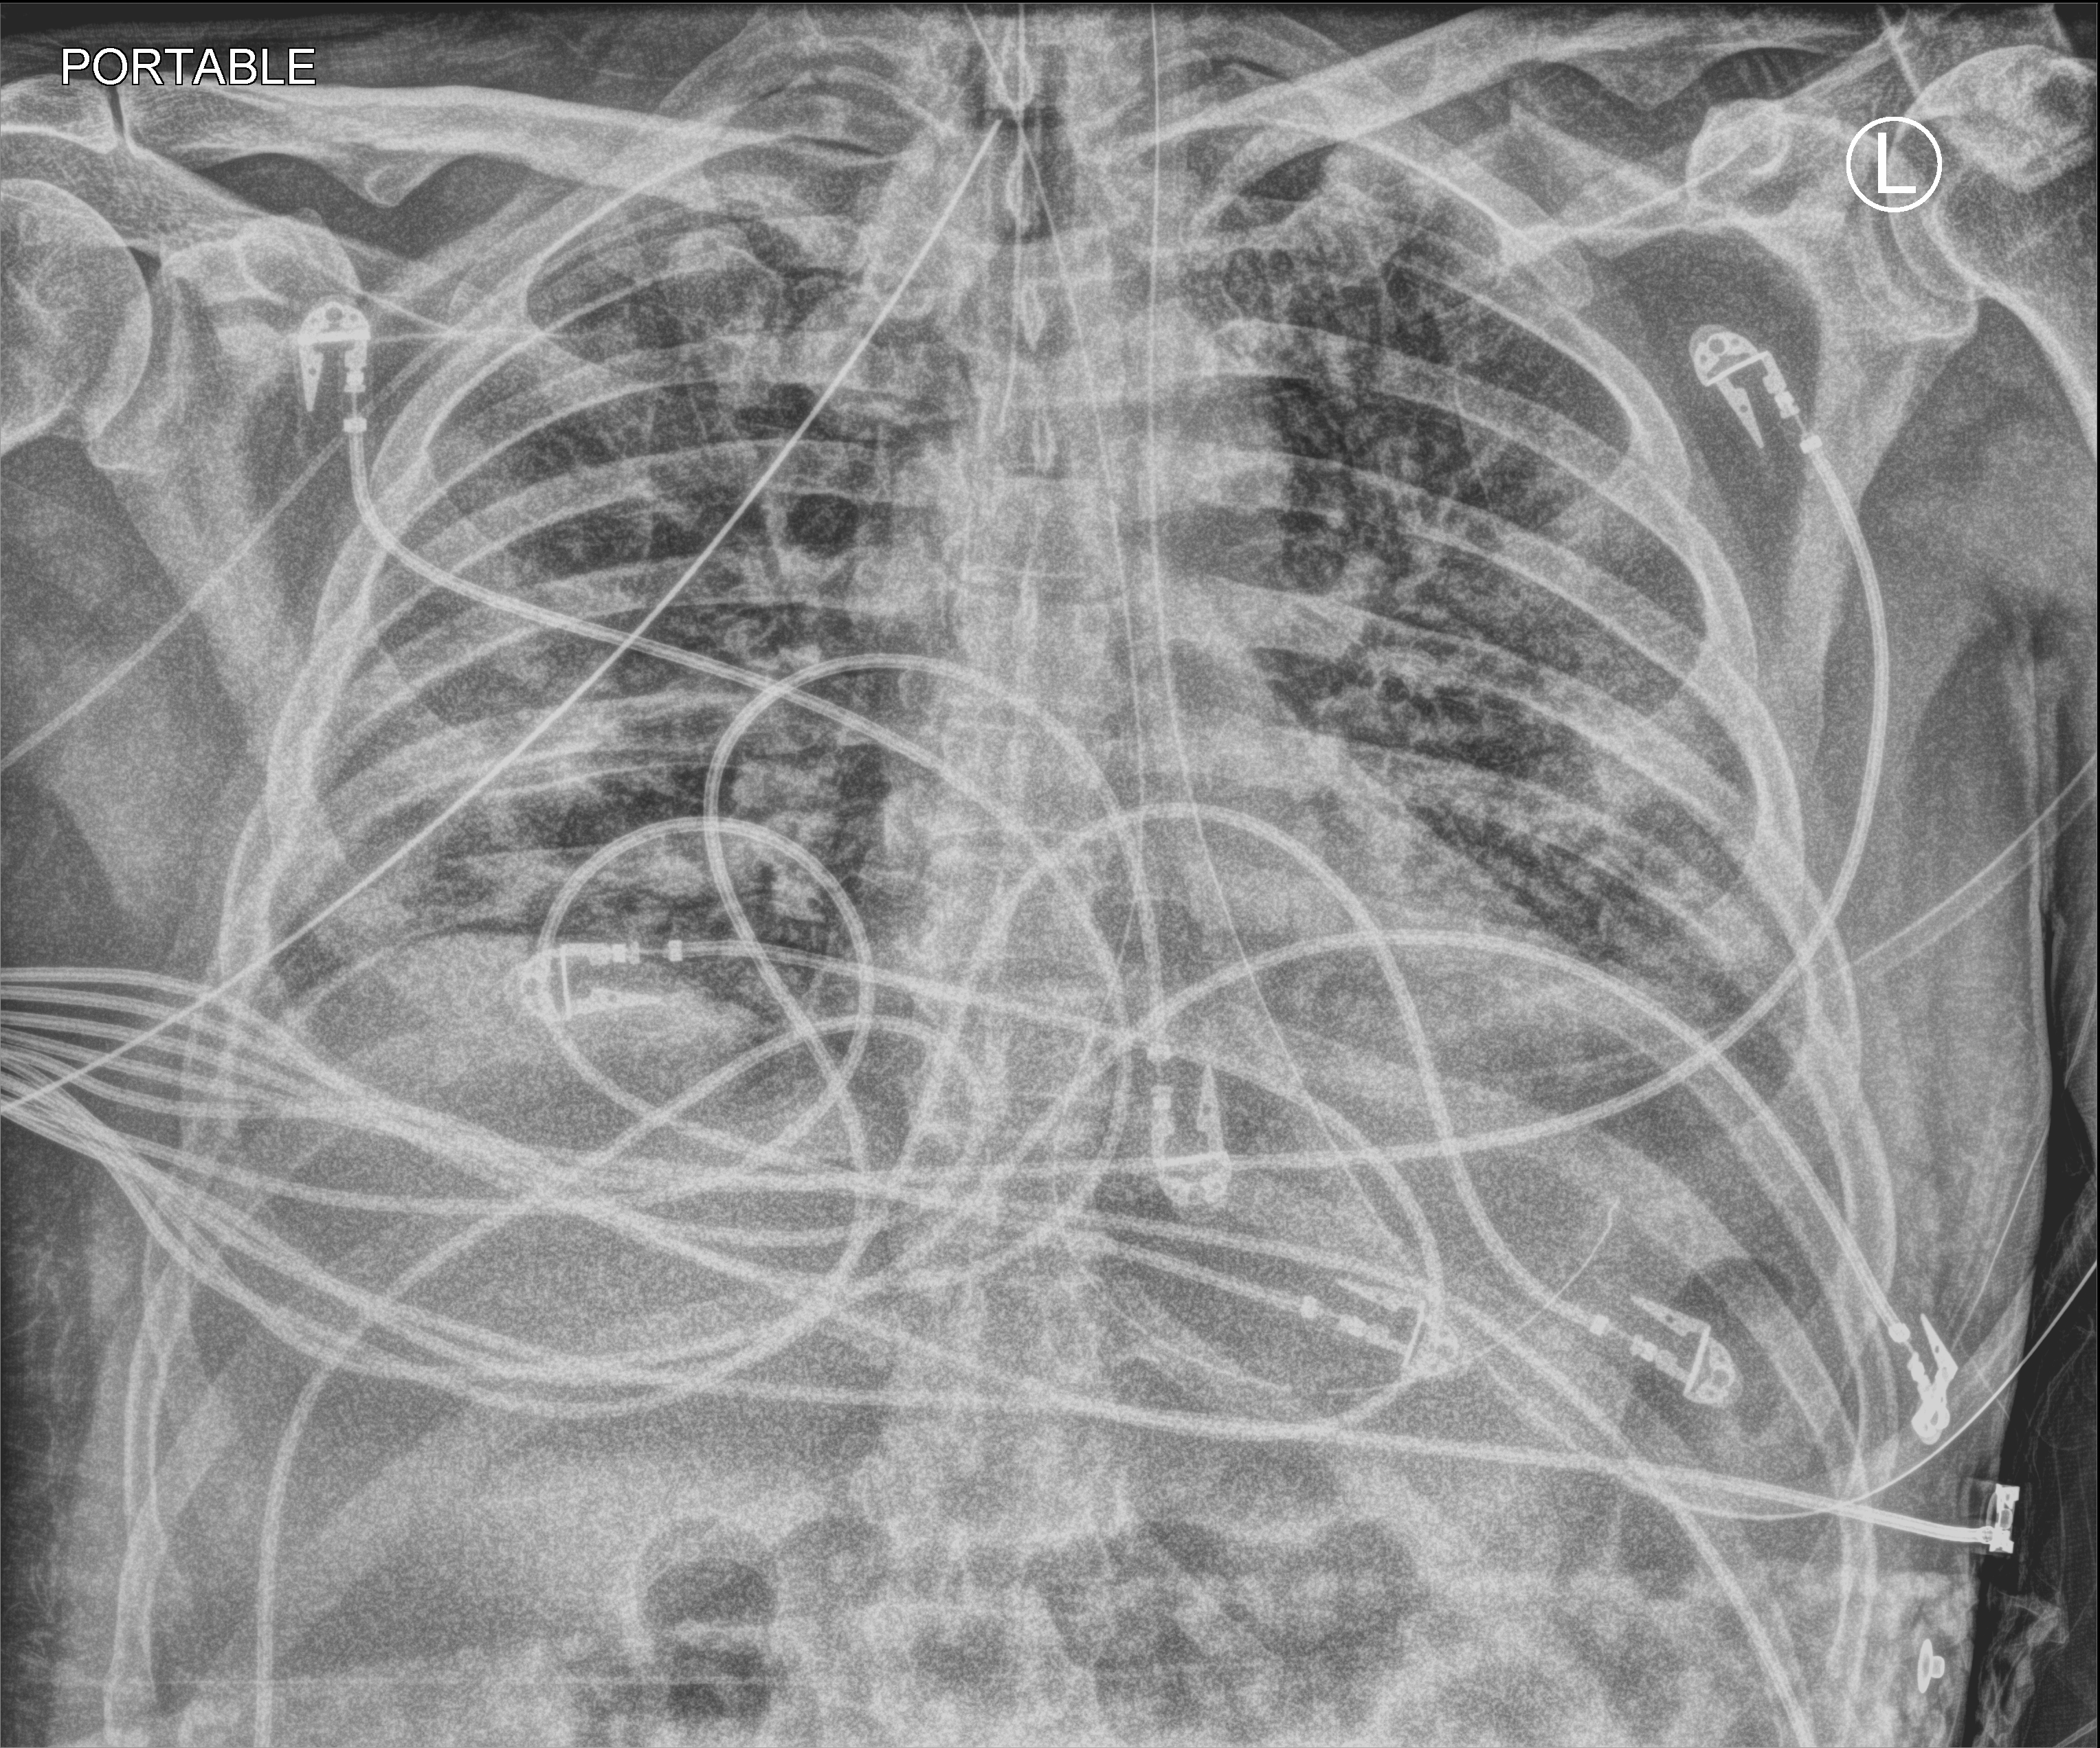
Bedside chest radiograph (computed radiography); anteroposterior (AP) projection. Patient hospitalised with COVID-19; male, aged 60–74 years.
Hospital-stay facts (about this admission, not read from this image; timing relative to this image not recorded): mechanically ventilated during this hospital stay: yes; admitted to intensive care during this hospital stay: yes.